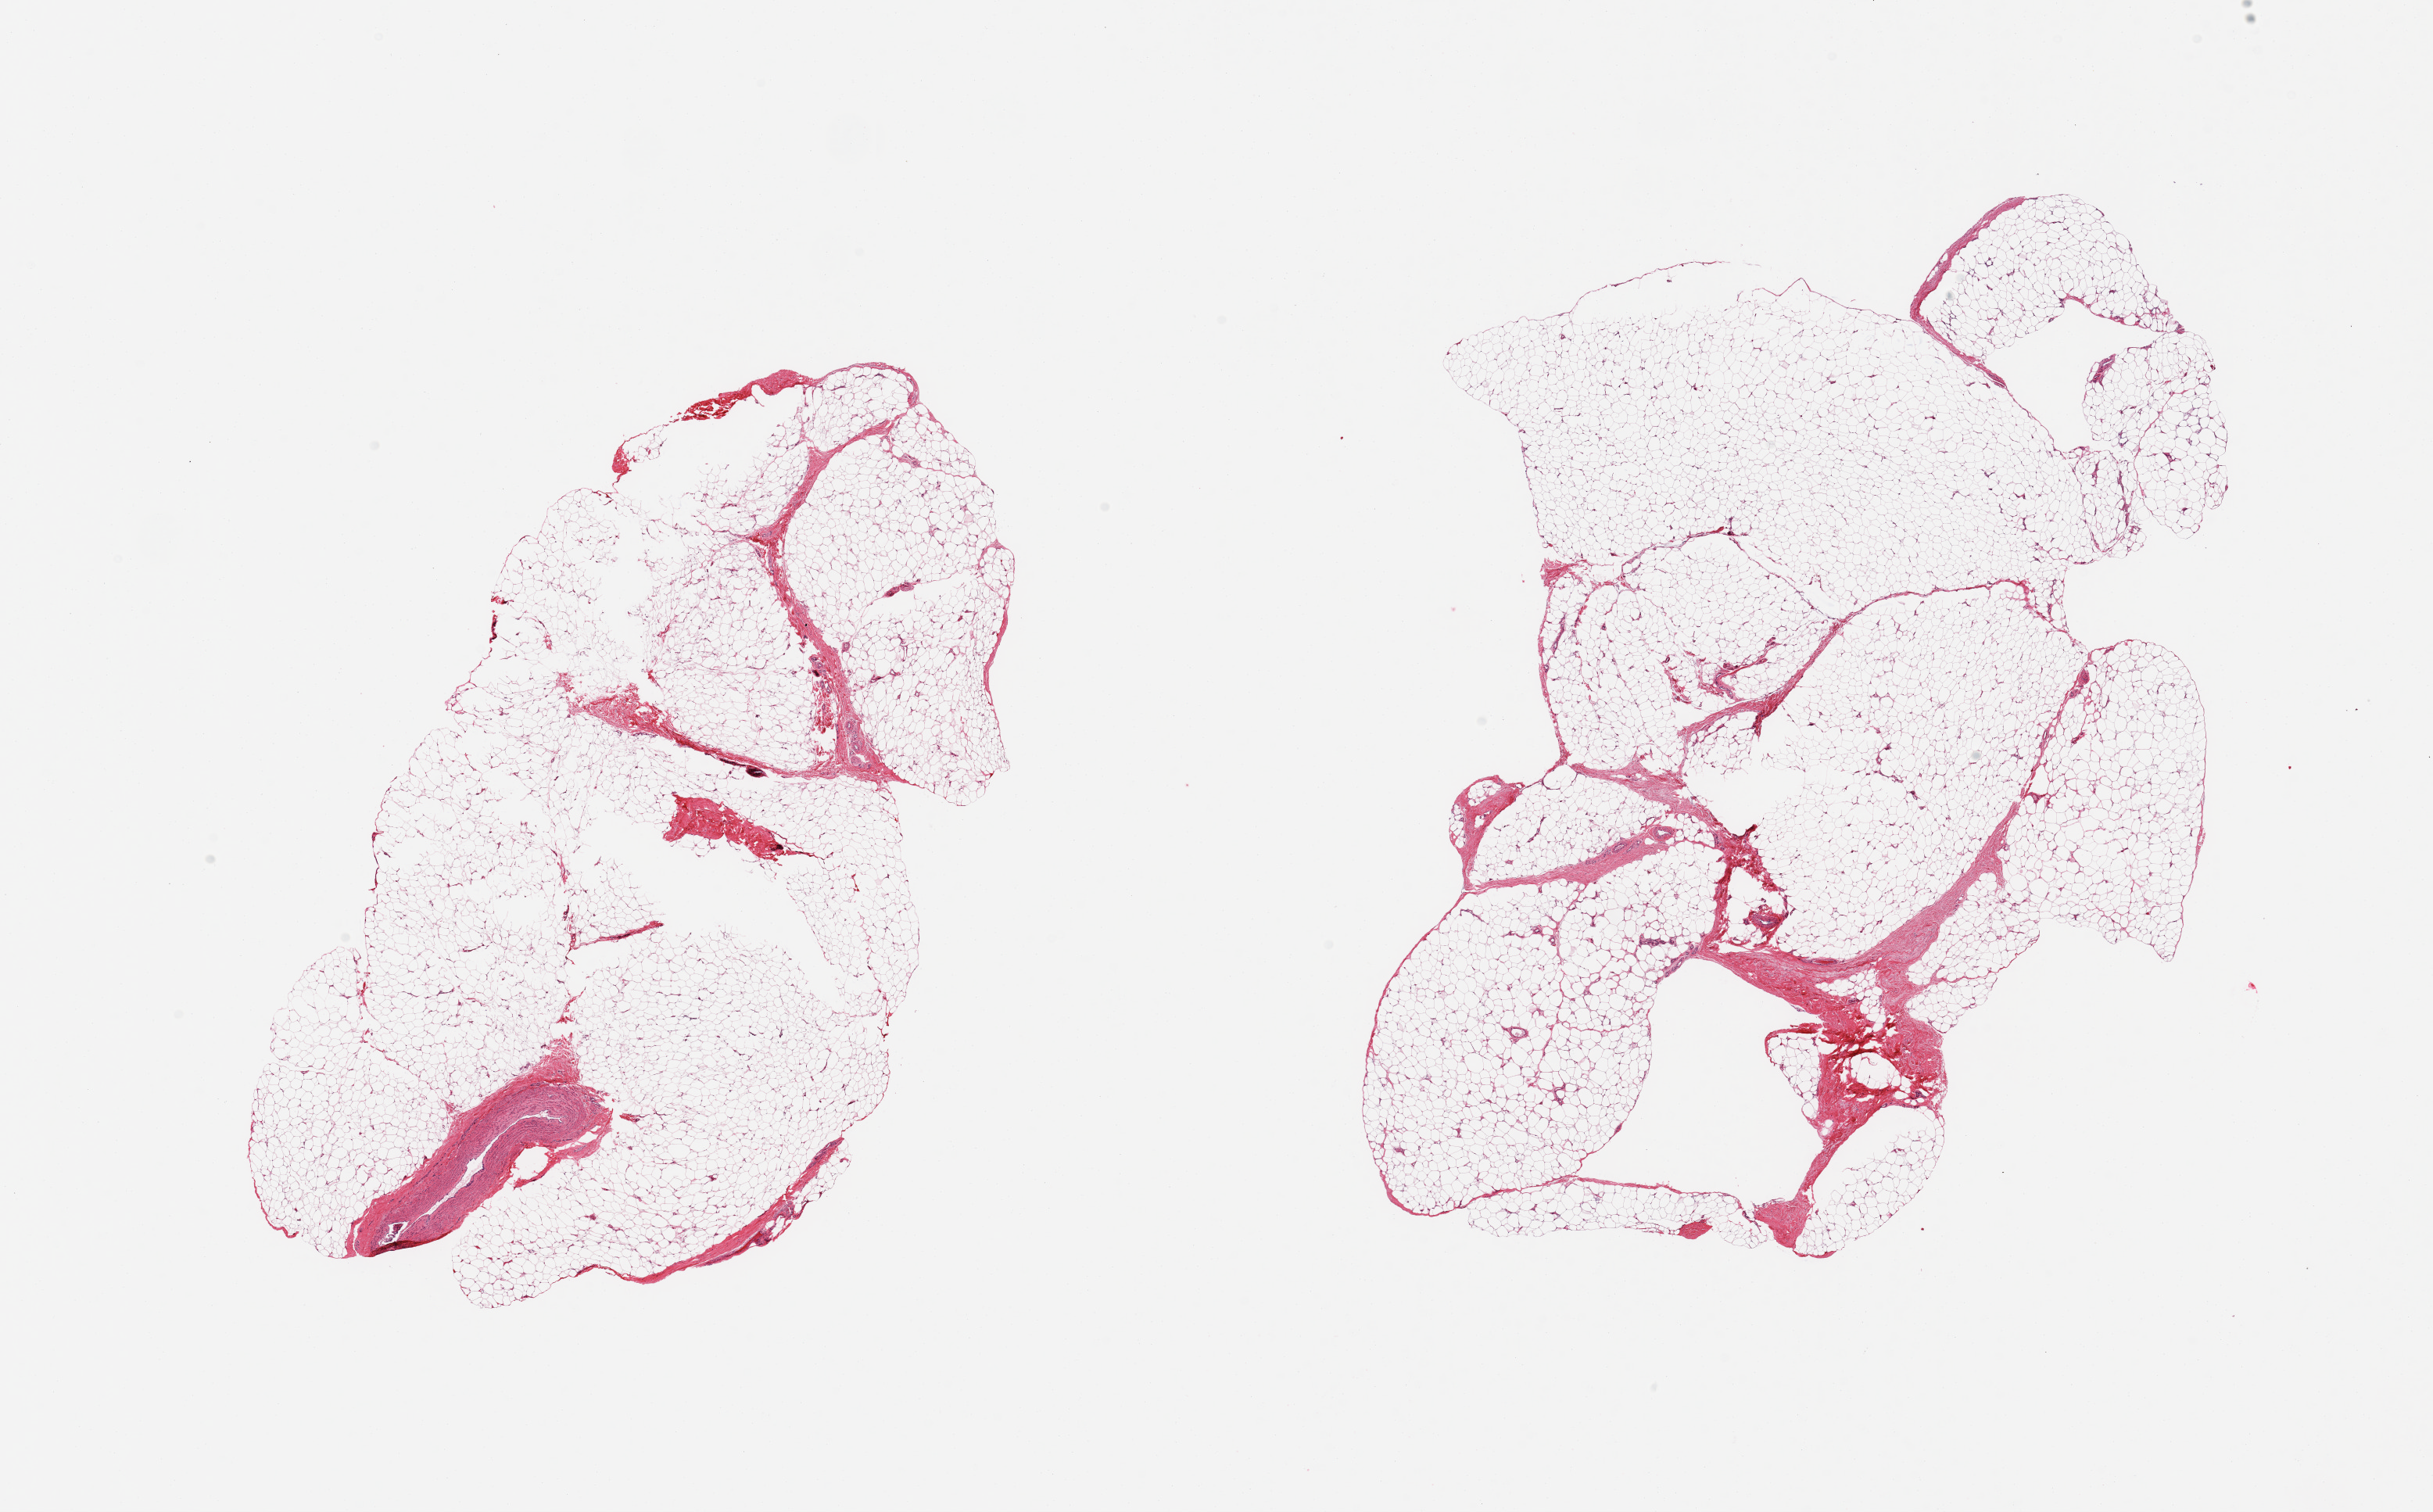
Digitized H&E-stained section — a low-resolution overview of the entire scanned area, about 24.6 x 15.3 mm (acquisition: 20x scan); PAXgene-fixed, paraffin-embedded tissue; target tissue: adipose tissue; donor tissue sample. Donor sex: male.
- review note (as recorded): 2 pieces; mature adipose tissue with 5-10% fibrous tissue/large vessel